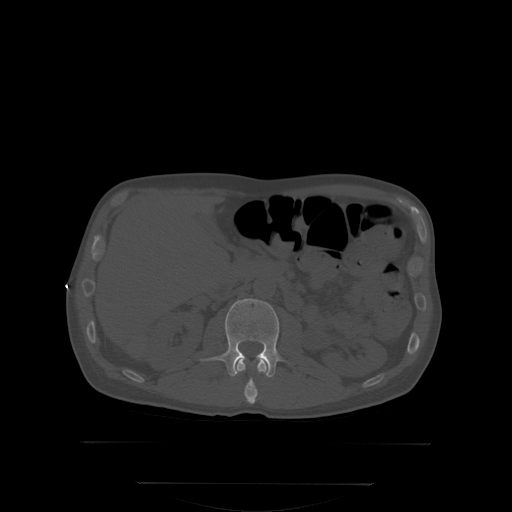
CT including the spine, one axial slice. Slice 142 of 350 in the series (ordered by position). Bone window (W 1800 / L 400 HU). 512 × 512 image matrix, field of view 500 × 500 mm. Male patient, age 58 years. From the clinical record (not read from this slice): primary cancer: prostate.
Annotated regions visible in this slice (semi-automatic segmentation, software-assisted and operator-edited):
- L1 vertebra: bounding box (x1, y1, x2, y2) in pixels: (237, 359, 268, 403)
- L2 vertebra: (221, 298, 280, 376)